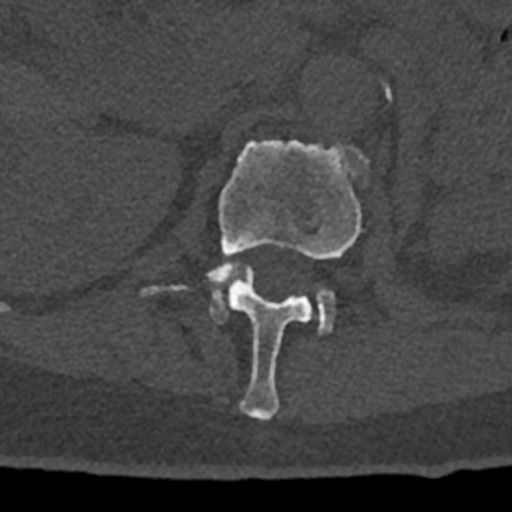
CT including the spine, one axial slice; position 423 of 797 along the scan axis; reconstruction kernel Br40s/3; 120 kVp; bone window (W 1800 / L 400 HU); 0.5 mm slice thickness; 512 × 512 image matrix, field of view 160 × 160 mm. Male patient, age 74 years. From the clinical record (not read from this slice): primary cancer: renal; vertebrae with lytic lesions (as recorded): T10, L1, L2, L3, L4, L5.
Structures marked on this image (semi-automatically segmented with operator editing):
- L1 vertebra: bounding box (x1, y1, x2, y2) in pixels: (142, 139, 369, 421)
- L2 vertebra: (210, 265, 335, 334)